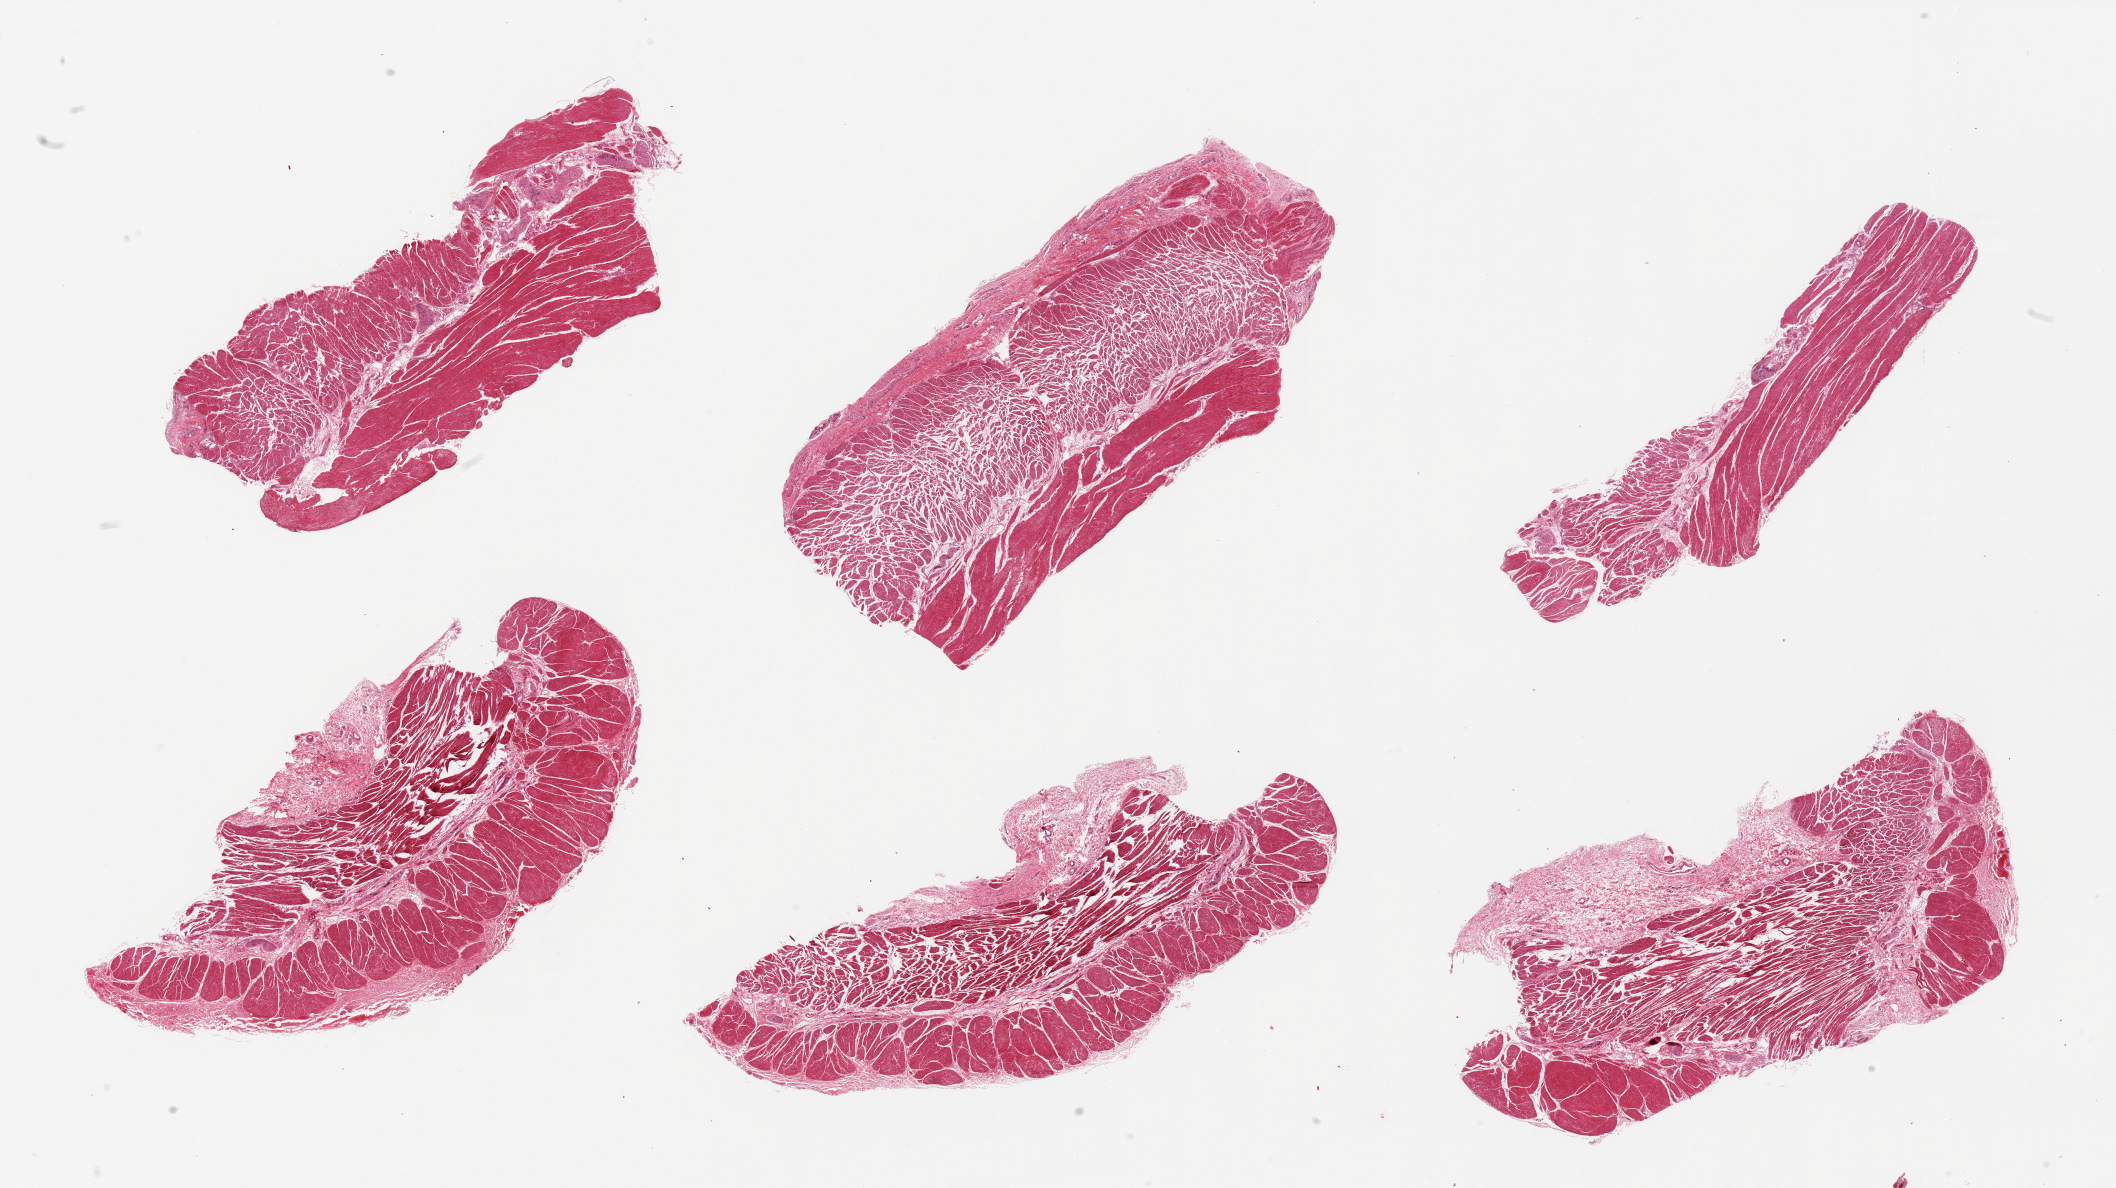
Digitized H&E-stained section, shown as a low-resolution overview of the whole scanned area (about 33.5 x 18.8 mm). PAXgene-fixed, paraffin-embedded tissue. Section of esophageal muscle (target tissue). Tissue donor sample. Male donor.
• pathologist's review note for this sample: 6 pieces; well trimmed